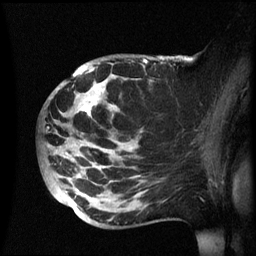
Breast MRI (dynamic contrast-enhanced), one sagittal slice; slice 35 of 60 in the series (ordered by position); dynamic contrast-enhanced series, image 2 of 3 at this slice position (ordered by acquisition); 1.5 T; TE 4.2 ms, TR 8.4 ms; 2.4 mm slice thickness; 256 × 256 image matrix, field of view 230 × 230 mm. Patient: female, 49 years.
Annotated regions visible in this slice (semi-automatic segmentation, software-assisted and operator-edited):
- analysis volume of interest (the breast-tissue region the enhancement analysis was run in; not a lesion): bounding box [x1, y1, x2, y2] px = [41, 55, 174, 229]
- tumour enhancement mask (voxels above the 70 % enhancement threshold inside the analysis volume of interest): [78, 60, 147, 149]